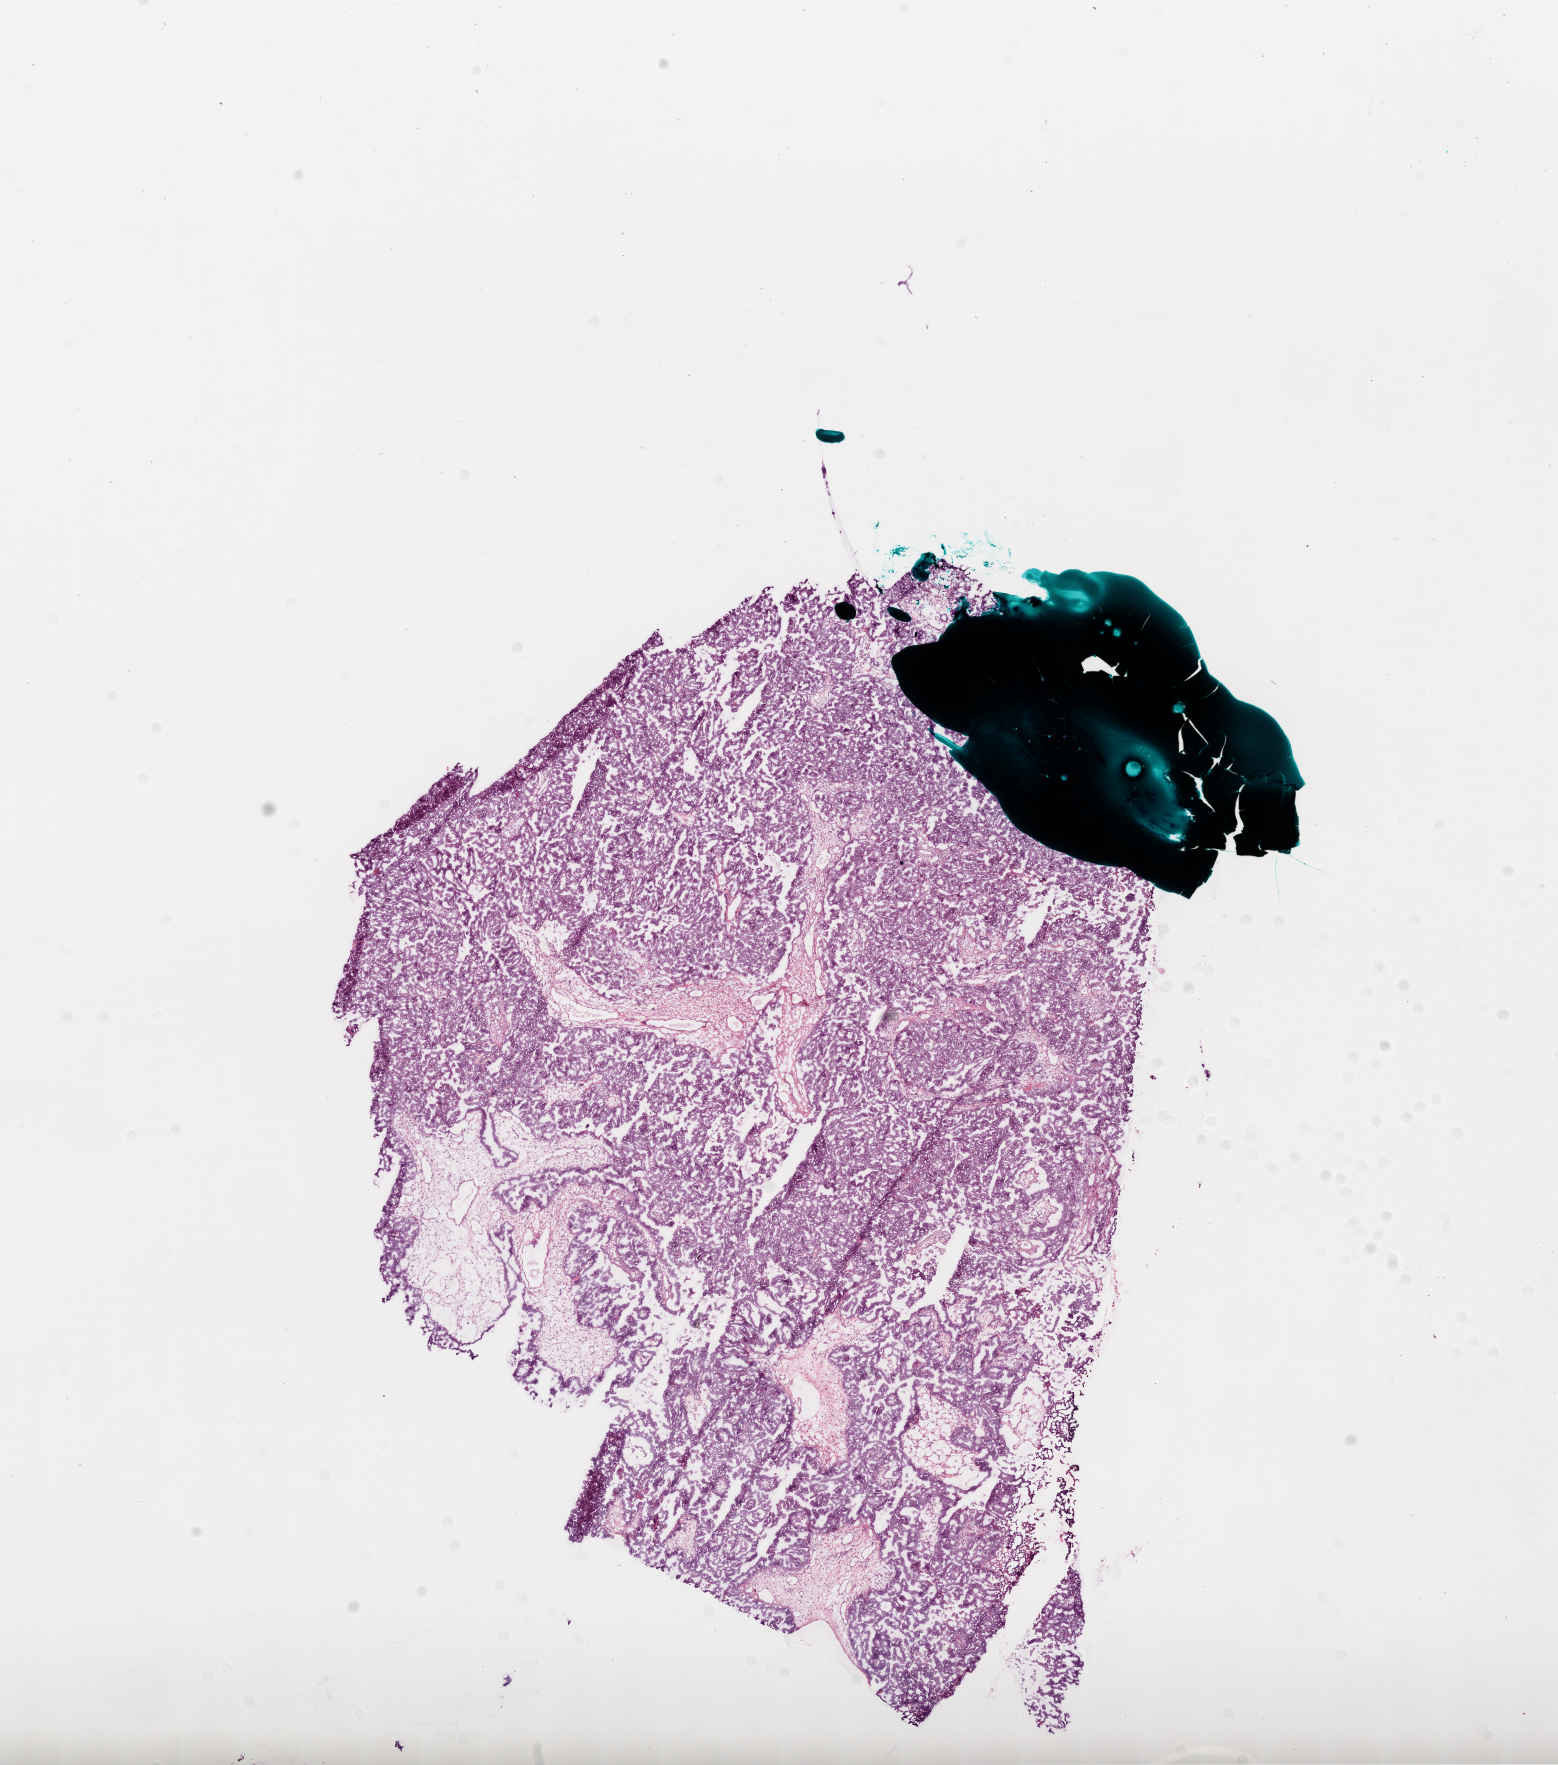
Digitized Hematoxylin and eosin (H&E) stained tissue section (whole slide), a low-resolution overview of the entire scanned area, about 12.6 x 14.2 mm; frozen section; sample: primary tumour, ovary. Patient: female, age at initial diagnosis 71 years. Histologic grade: G3 (poorly differentiated). Pathologist review of this section (percent, as recorded): tumour cells 90%, tumour nuclei 95%, normal cells 5%, stromal cells 5%, necrosis 0%.
* FIGO stage: IIIC
* diagnosis: Serous cystadenocarcinoma, NOS